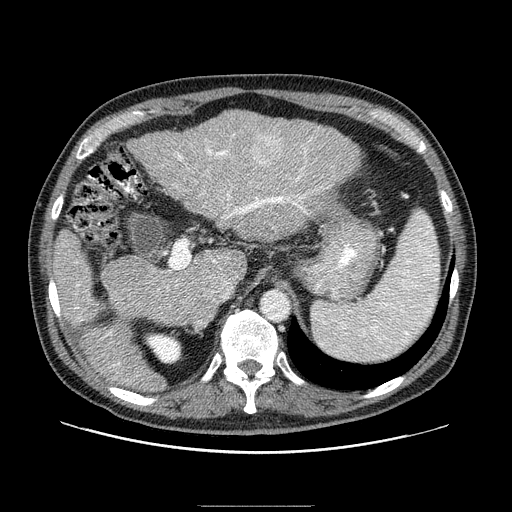
Contrast-enhanced abdominal CT (liver protocol), one axial slice; position 55 of 99 along the scan axis; reconstruction kernel STANDARD; 100 kVp; one of 2 acquisitions stored at this slice position; soft-tissue window (W 400 / L 40 HU); 512 × 512 image matrix, field of view 400 × 400 mm. From the clinical record (not read from this slice): diagnosis: hepatocellular carcinoma (patient treated with transarterial chemoembolisation; whether this scan precedes or follows treatment is not stated here); TNM stage (as recorded): Stage-II; Child-Pugh class: A; tumour differentiation: well differentiated; tumour nodularity: multinodular.
Annotated regions visible in this slice (semi-automatic segmentation, software-assisted and operator-edited):
- liver parenchyma outside the tumour (the mass and vessels are separate outlines, so this box may not span the whole liver): bounding box [x1, y1, x2, y2] px = [52, 110, 360, 390]
- mass: [250, 131, 286, 169]
- liver vessels: [76, 134, 312, 367]